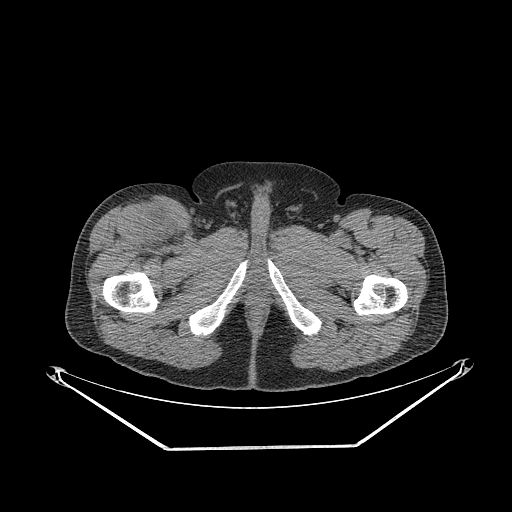
CT of an extremity soft-tissue mass (from a PET/CT study), one axial slice; 140 kVp; soft-tissue window (W 400 / L 40 HU); 512 × 512 image matrix, field of view 500 × 500 mm. Male patient. From the clinical record (not read from this slice): histological type: pleiomorphic leiomyosarcoma; grade: intermediate; site of the primary tumour: right thigh.
Outlined on this slice (expert contour drawn on MRI and transferred to this co-registered scan by the dataset authors):
- gross tumour volume including surrounding oedema: box from (x=137, y=203) to (x=177, y=247) px
- gross tumour volume (mass): (x=144, y=212)–(x=175, y=243)